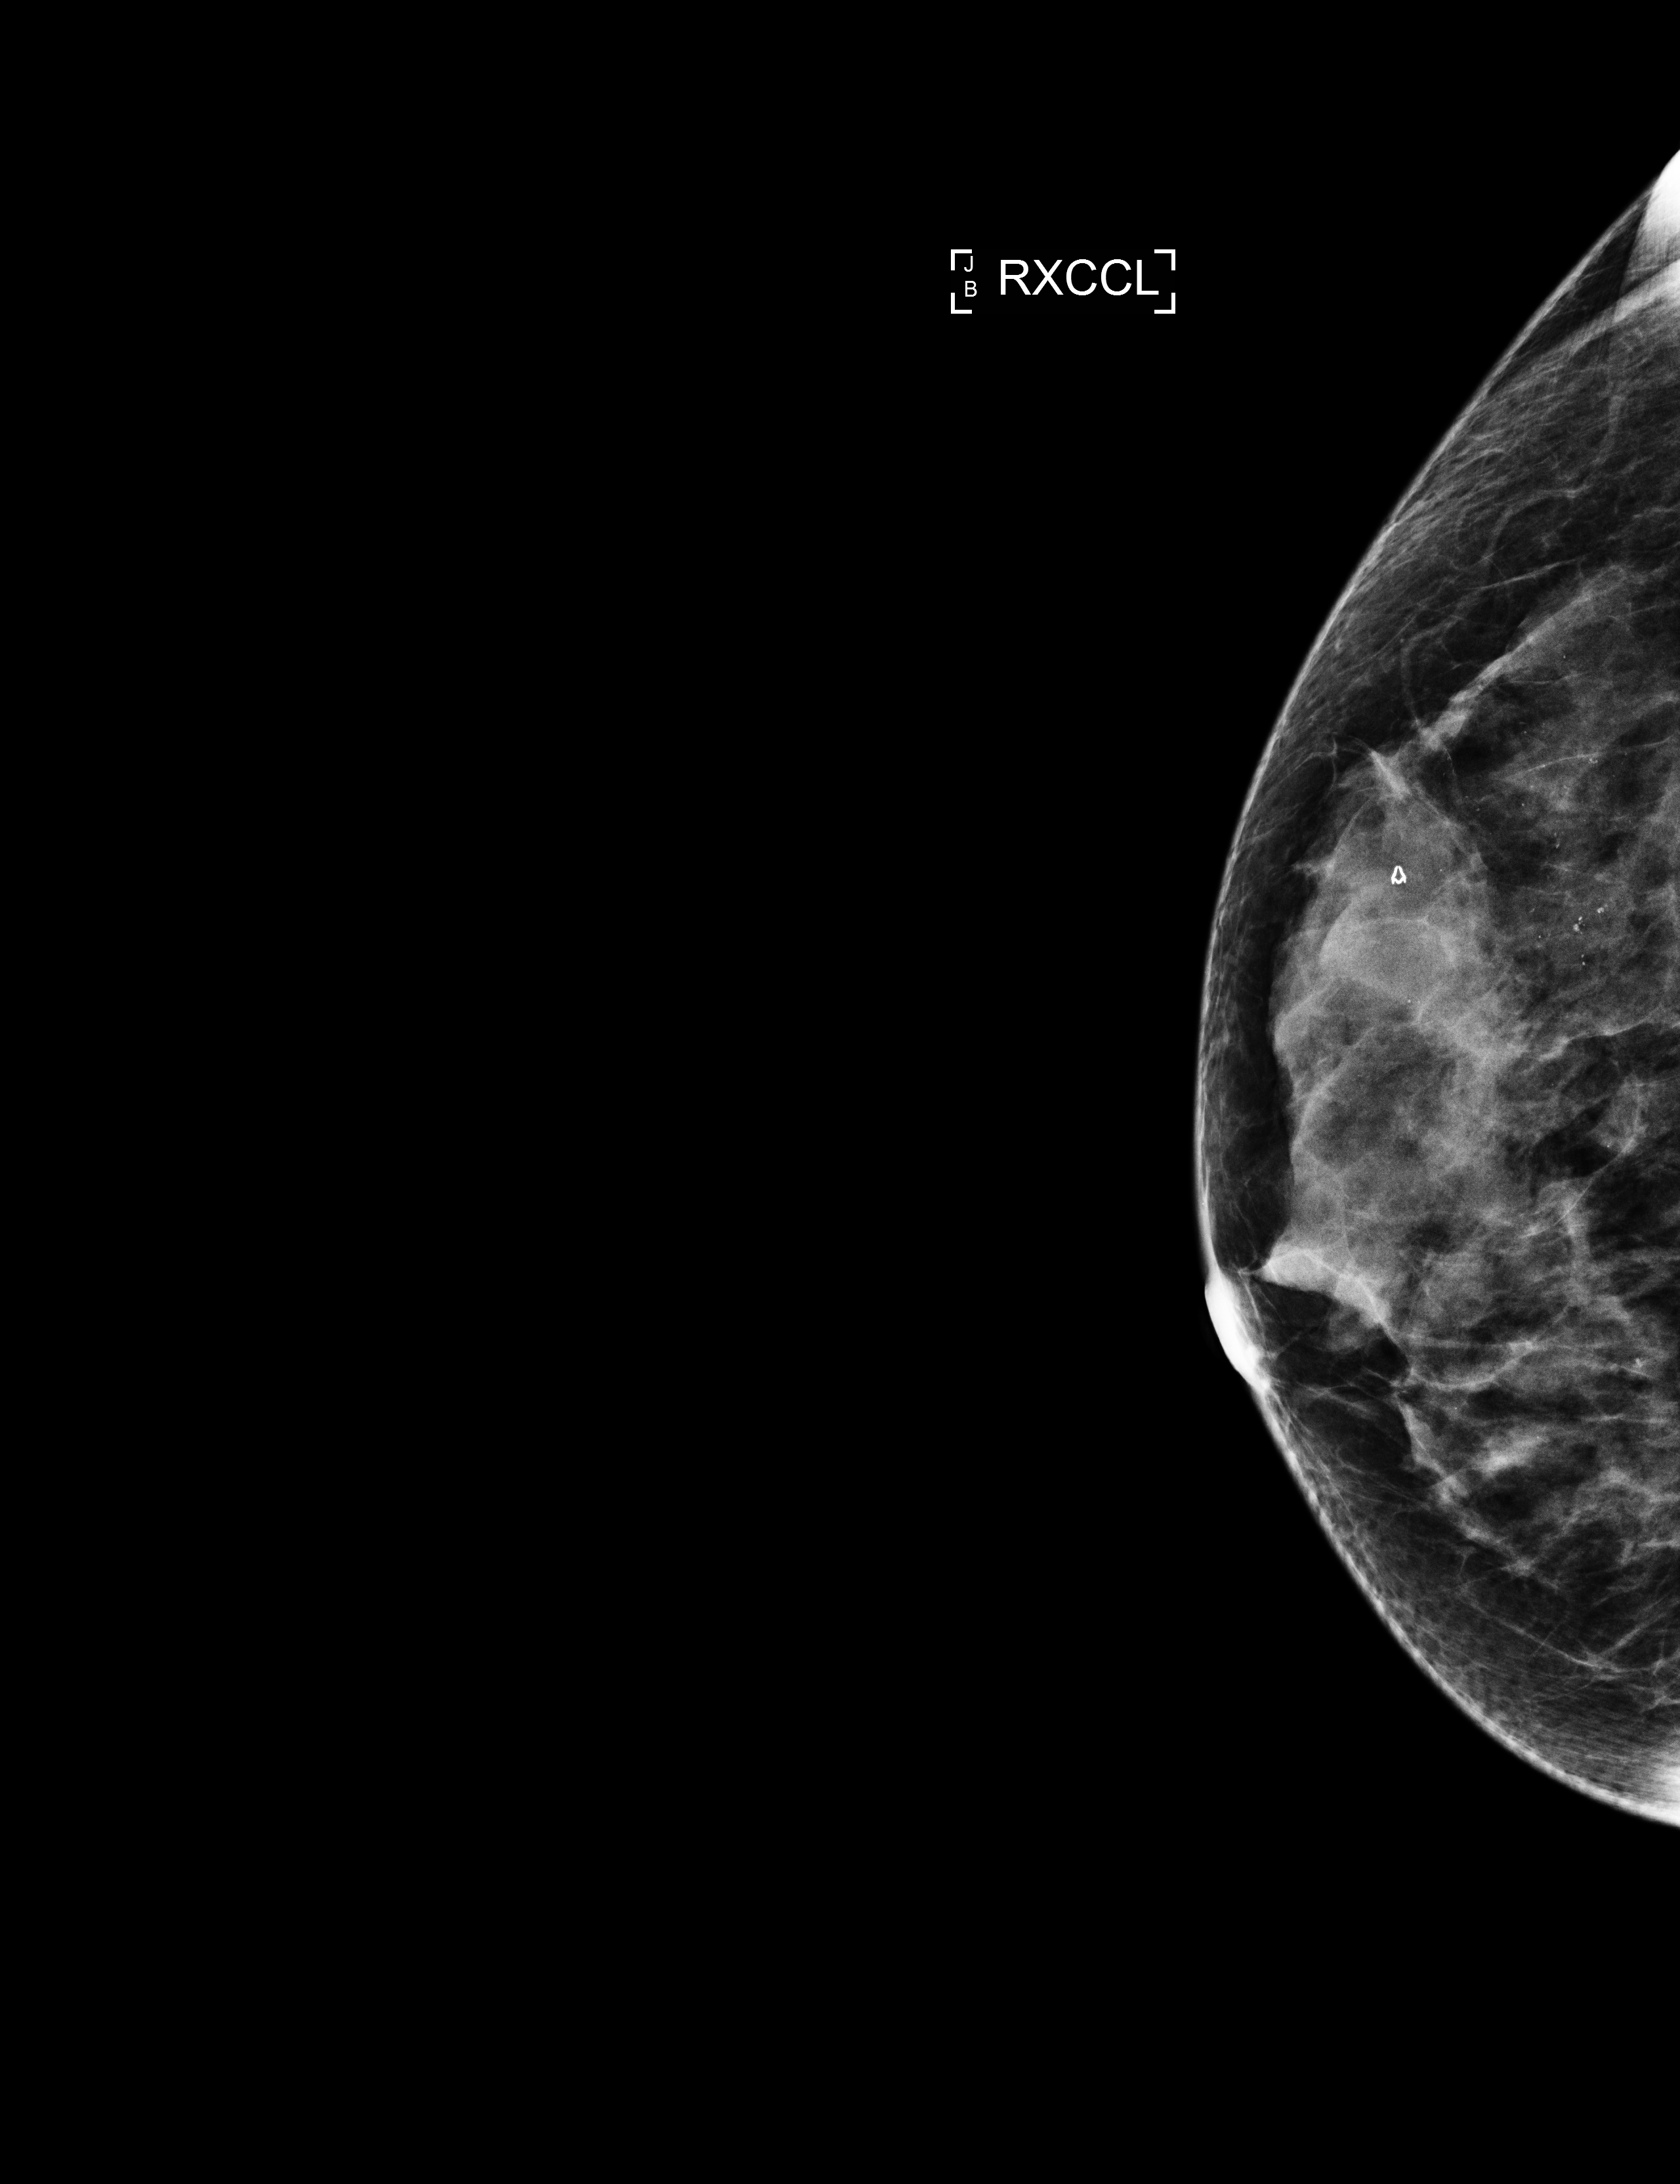
Full-field digital mammogram (FFDM), right breast, exaggerated CC view (lateral), annual screening mammography examination, system: Selenia Dimensions. Patient: female, 58 years.
- BI-RADS breast density category at the screening exam (both breasts, scale 1–4): 3
- final BI-RADS category for the screening round (tomosynthesis exam, both breasts): category 1
- recall: no recall after this screen